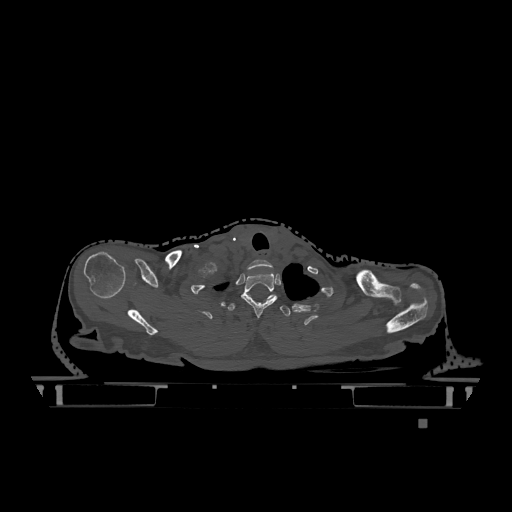
CT including the spine, one axial slice; slice 992 of 1317 in the series (ordered by position); bone window (W 1800 / L 400 HU); 0.5 mm slice thickness; 512 × 512 image matrix, field of view 500 × 500 mm. Female patient, age 74 years. From the clinical record (not read from this slice): primary cancer: lung; vertebrae with lytic lesions (as recorded): T1, T4, T5, T6, L4, L5.
Annotated regions visible in this slice (semi-automatic segmentation, software-assisted and operator-edited):
- T1 vertebra: bounding box [x1, y1, x2, y2] px = [241, 272, 278, 318]
- T2 vertebra: [228, 295, 291, 316]